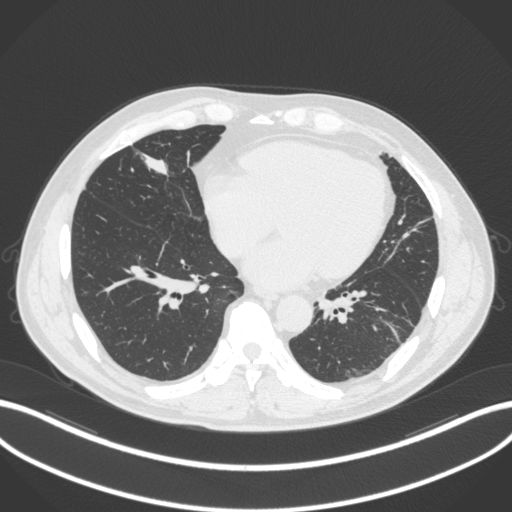
Chest CT, one axial slice; position 97 of 399 along the scan axis; reconstruction kernel B31f; lung window (W 1500 / L -600 HU); 512 × 512 image matrix. Patient: male, 59 years. Case-level facts recorded for this patient, not image findings: clinical TNM (as recorded): T2a N1 M0.
Outlined on this slice (rectangle marked by the reading radiologist):
- lung tumour (recorded histology: adenocarcinoma): bounding box (x1, y1, x2, y2) in pixels: (140, 146, 177, 178)